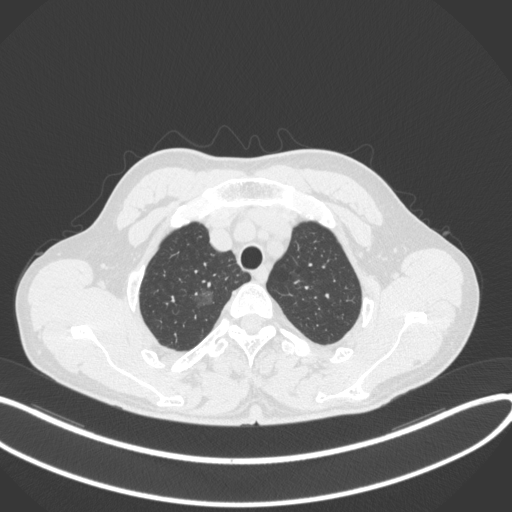
Chest CT, one axial slice; position 320 of 407 along the scan axis; 120 kVp; lung window (W 1500 / L -600 HU); 1 mm slice thickness; 512 × 512 image matrix, field of view 400 × 400 mm. Male patient, age 58 years. Case-level facts recorded for this patient, not image findings: clinical TNM (as recorded): T1c N0 M0; histopathological grade: G1-2.
Structures marked on this image (rectangle marked by the reading radiologist):
- lung tumour (recorded histology: adenocarcinoma): bounding box <189,281,223,311> (left, top, right, bottom; pixels)